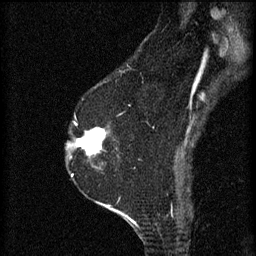
Breast MRI (dynamic contrast-enhanced), one sagittal slice. Slice 43 of 60 in the series (ordered by position). 3 images stored at this slice position (order not interpretable as contrast timing). 1.5 T. TE 4.2 ms, TR 8.2 ms. 2 mm slice thickness. 256 × 256 image matrix, field of view 180 × 180 mm. Female patient, age 60 years.
Annotated regions visible in this slice (semi-automatic segmentation, software-assisted and operator-edited):
- analysis volume of interest (the breast-tissue region the enhancement analysis was run in; not a lesion): box from (x=74, y=124) to (x=111, y=159) px
- tumour enhancement mask (voxels above the 70 % enhancement threshold inside the analysis volume of interest): (x=76, y=124)–(x=105, y=155)